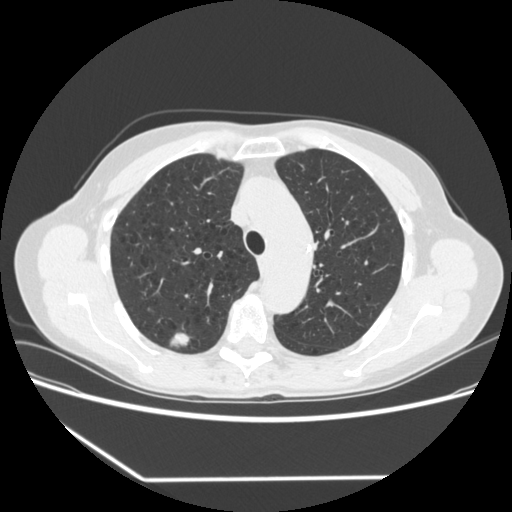
Low-dose screening chest CT, one axial slice. Slice 247 of 323 in the series (ordered by position). 120 kVp. Lung window (W 1500 / L -600 HU). 1.25 mm slice thickness. 512 × 512 image matrix, field of view 360 × 360 mm.
Structures marked on this image (outlined manually by an expert reader):
- lesion 1 (tumor, upper lobe of right lung): bounding box (x1, y1, x2, y2) in pixels: (170, 333, 190, 347)